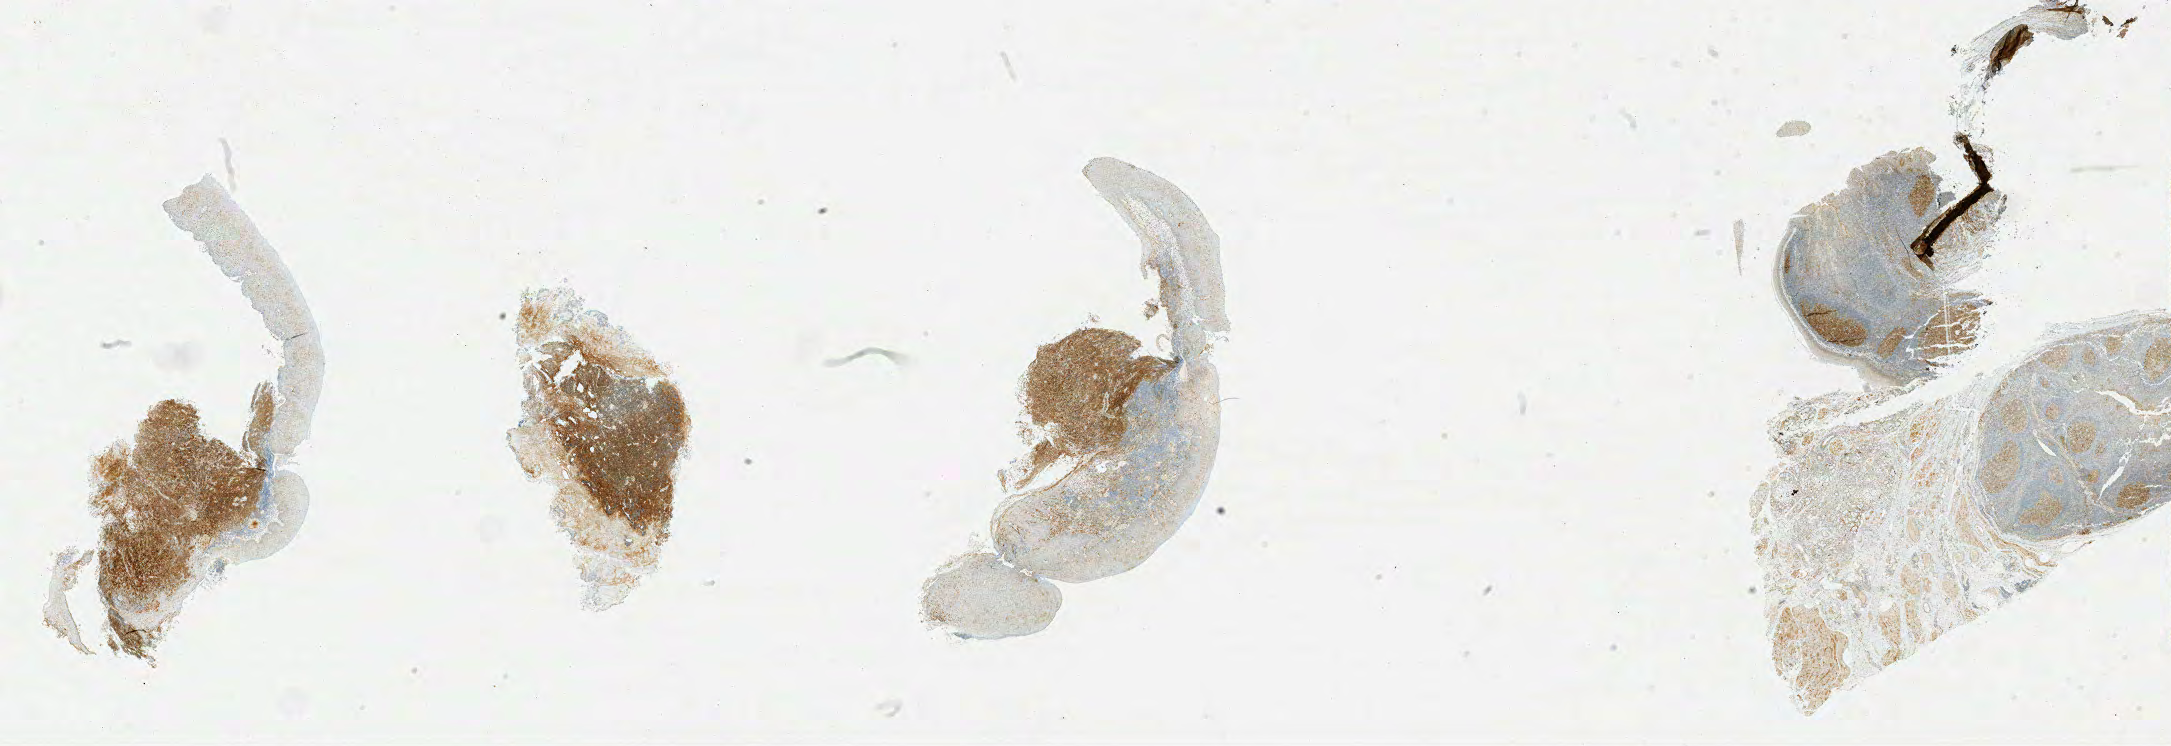
Immunohistochemistry (IHC) whole-slide image stained for CD10 — low-resolution overview of the scanned area, about 34.6 x 11.9 mm; tumor tissue. Patient: male, age 66 years.
Histologic diagnosis: Burkitt lymphoma, NOS.